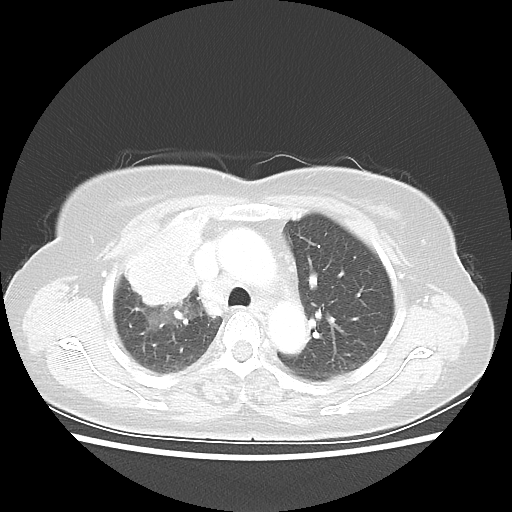
Chest CT, one axial slice. Lung window (W 1500 / L -600 HU). 5 mm slice thickness. 512 × 512 image matrix, field of view 337 × 337 mm. Patient: female, 62 years. Case-level facts recorded for this patient, not image findings: clinical TNM (as recorded): T4 N3 M0.
Annotated regions visible in this slice (bounding box drawn by a radiologist):
- lung tumour (recorded histology: squamous cell carcinoma): box from (x=117, y=210) to (x=219, y=306) px